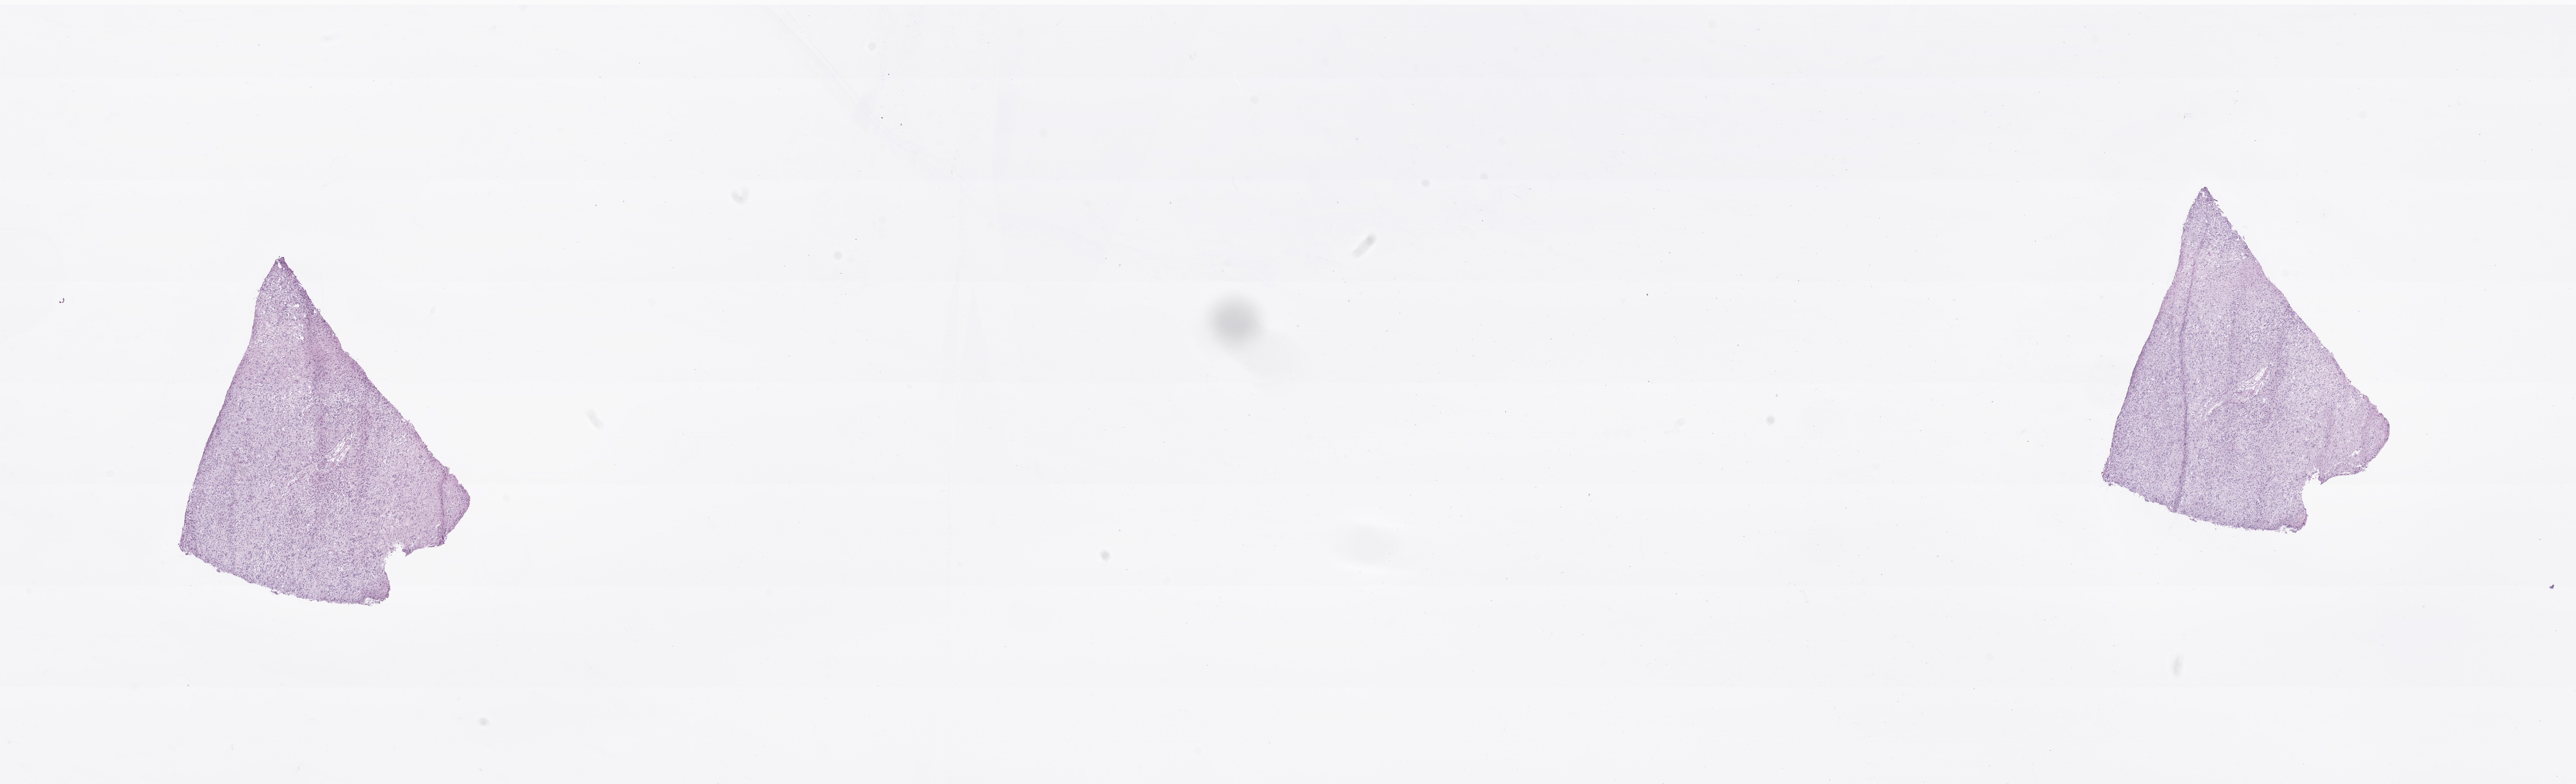
Digitized hematoxylin and eosin (H&E)-stained section of tumor tissue from the frontal lobe — whole scanned area (about 27.0 x 8.2 mm) shown as a low-resolution overview, frozen section. Patient male; age 63 months (5 years 3 months).
Diagnosis: Glioma, malignant.